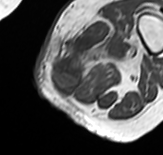
MRI of an extremity soft-tissue mass, one axial slice. Position 15 of 65 along the scan axis. MR volume resampled by the dataset authors to the PET/CT grid (not the native acquisition matrix). 3.27 mm slice thickness. 163 × 155 image matrix, field of view 159 × 151 mm. Female patient. Case-level facts recorded for this patient, not image findings: histological type: pleomorphic leiomyosarcoma; grade: high; site of the primary tumour: left thigh.
Outlined on this slice (expert contour drawn on MRI and transferred to this co-registered scan by the dataset authors):
- gross tumour volume including surrounding oedema: bounding box [x1, y1, x2, y2] px = [51, 24, 139, 93]
- gross tumour volume (mass): [53, 61, 82, 93]